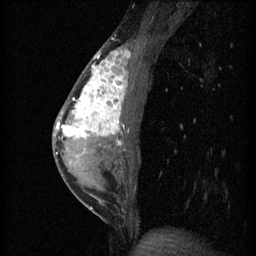
Breast MRI (dynamic contrast-enhanced), one sagittal slice. Position 26 of 60 along the scan axis. 3 images stored at this slice position (order not interpretable as contrast timing). 1.5 T. TE 4.2 ms, TR 11 ms. 2 mm slice thickness. 256 × 256 image matrix, field of view 180 × 180 mm. Female patient, age 40 years.
Outlined on this slice (semi-automatically segmented with operator editing):
- analysis volume of interest (the breast-tissue region the enhancement analysis was run in; not a lesion): bounding box [x1, y1, x2, y2] px = [55, 42, 140, 203]
- tumour enhancement mask (voxels above the 70 % enhancement threshold inside the analysis volume of interest): [57, 50, 131, 155]